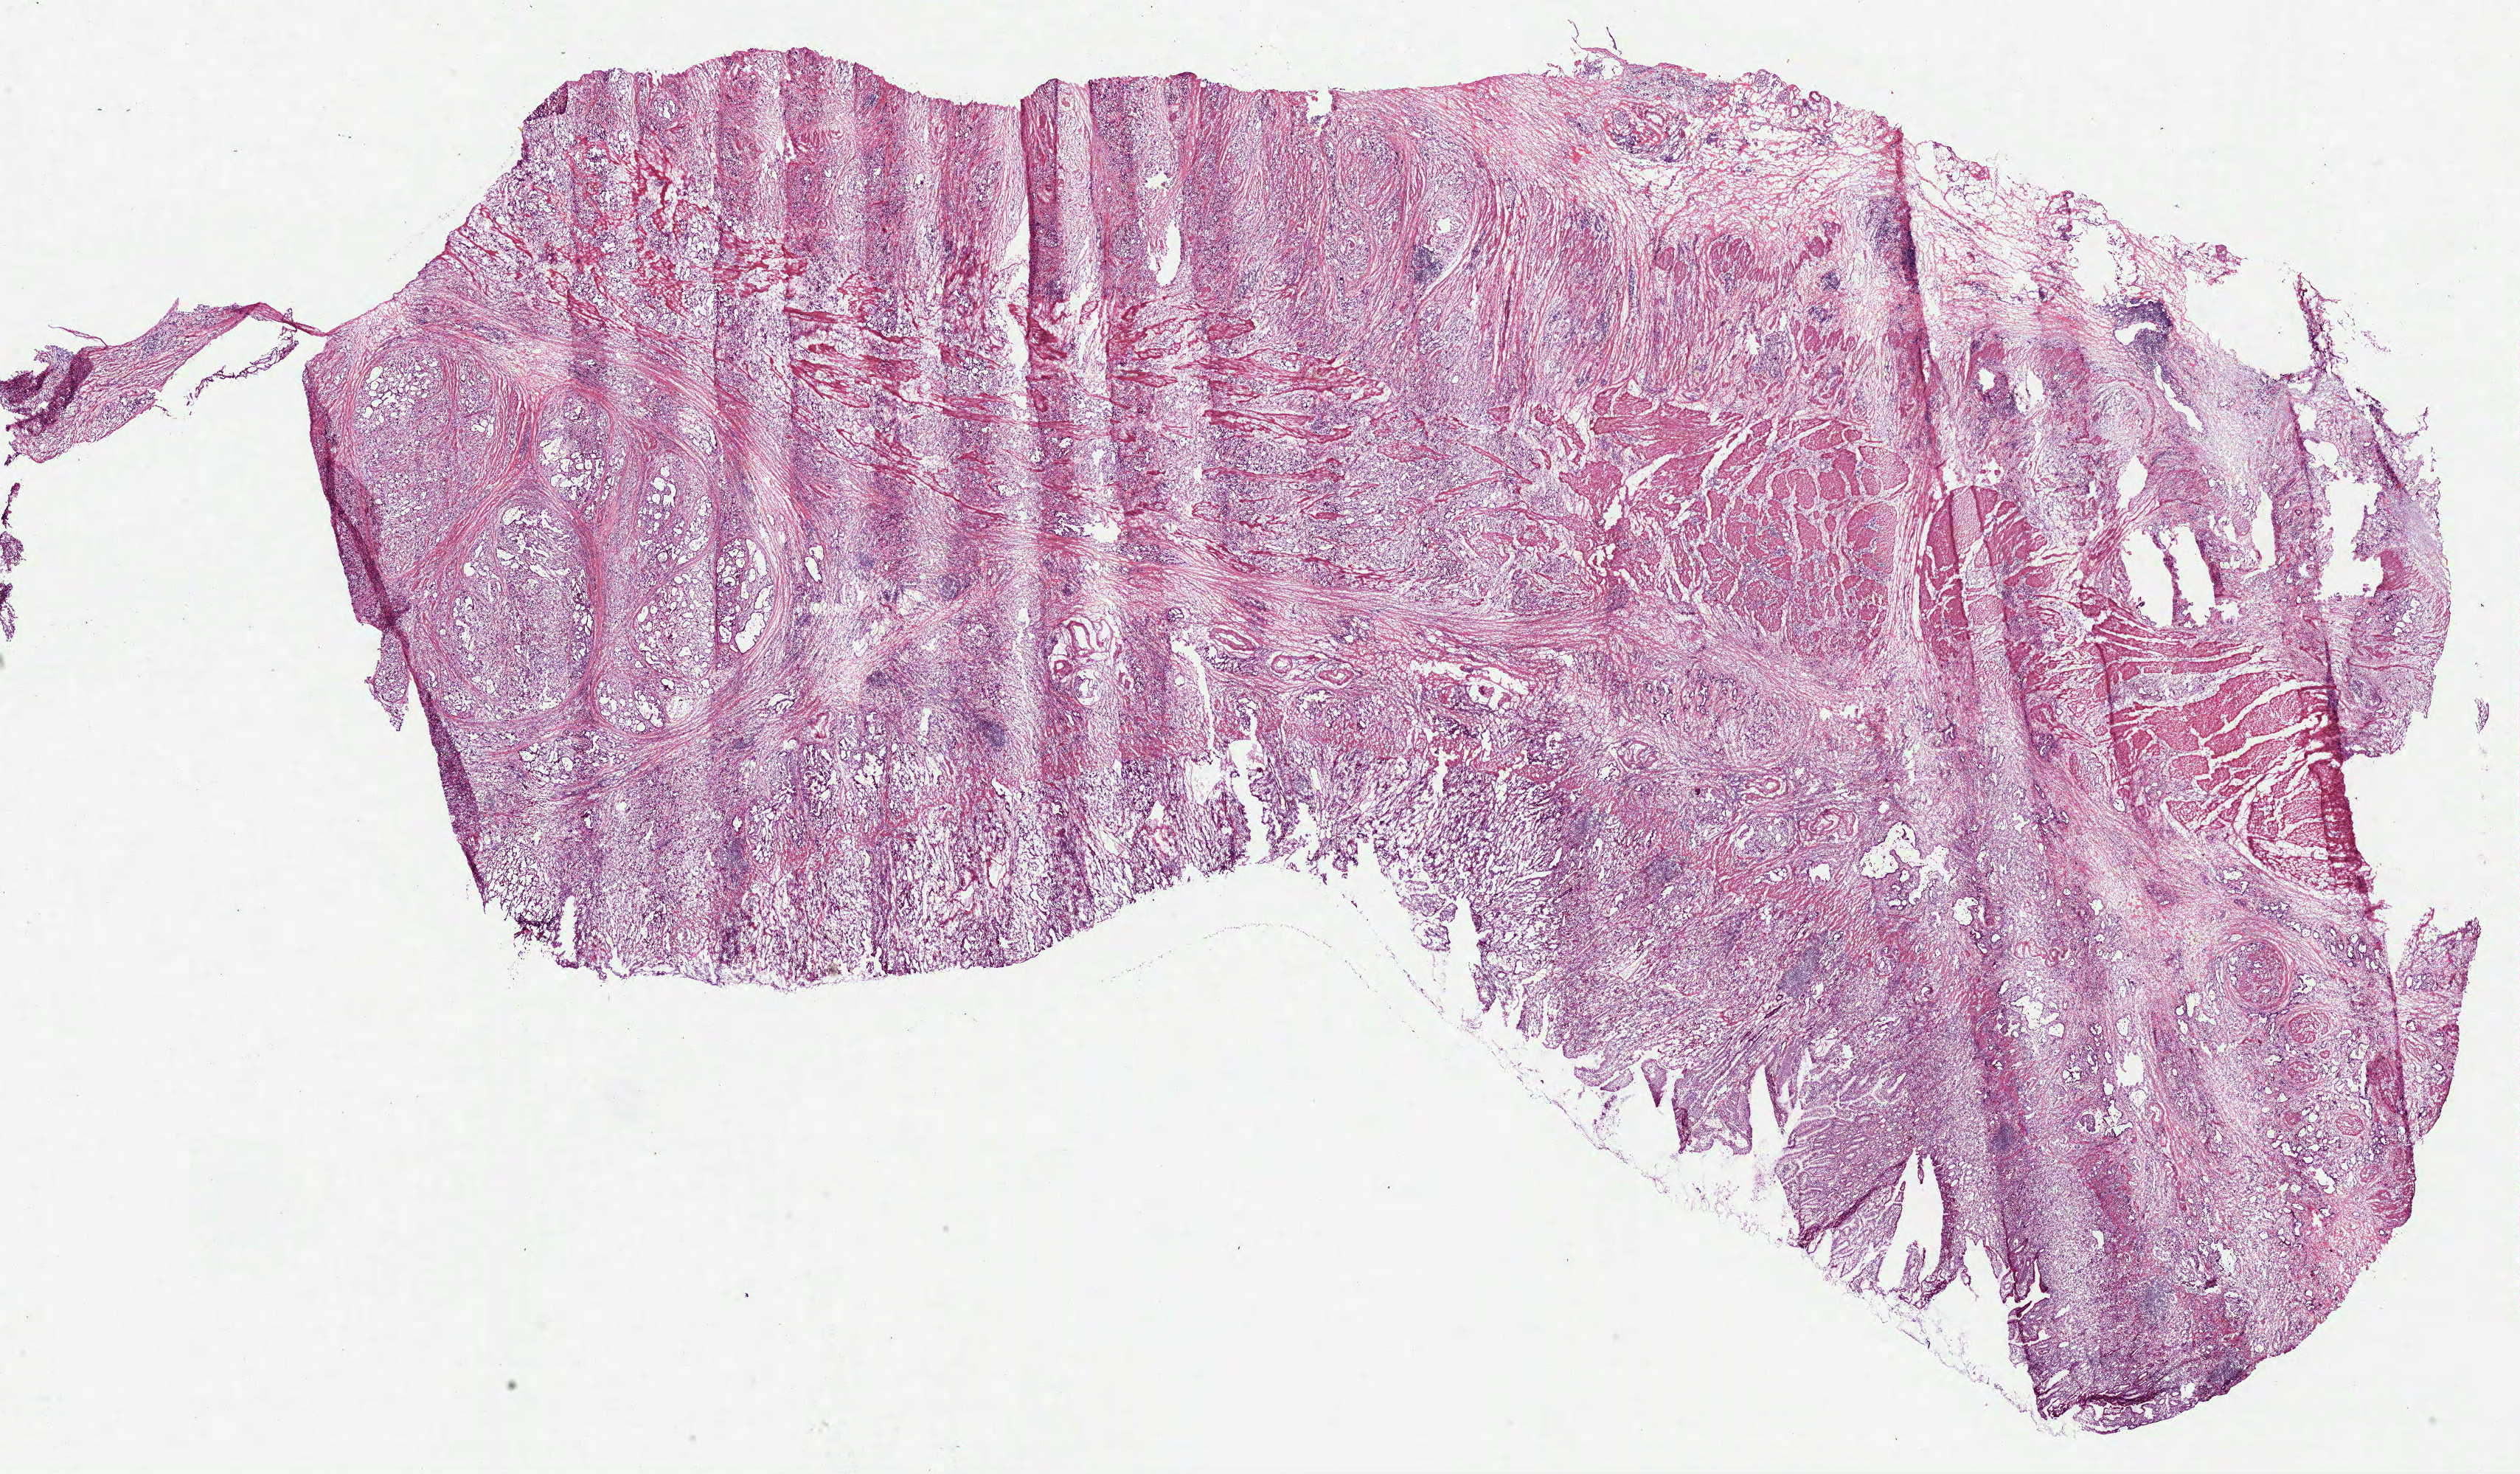
Digitized H&E-stained tissue section (whole slide), low-resolution overview of the scanned area, about 27.6 x 16.1 mm, frozen section, stomach, primary tumour sample. Patient: male, age at initial diagnosis 62 years. Histologic grade: G3 (poorly differentiated). Pathologist review of this section (percent, as recorded): tumour cells 65%, tumour nuclei 65%, normal cells 5%, stromal cells 30%, necrosis 0%.
AJCC pathologic stage: IIIC (7th edition). Pathologic diagnosis: Adenocarcinoma, NOS (fundus of stomach).